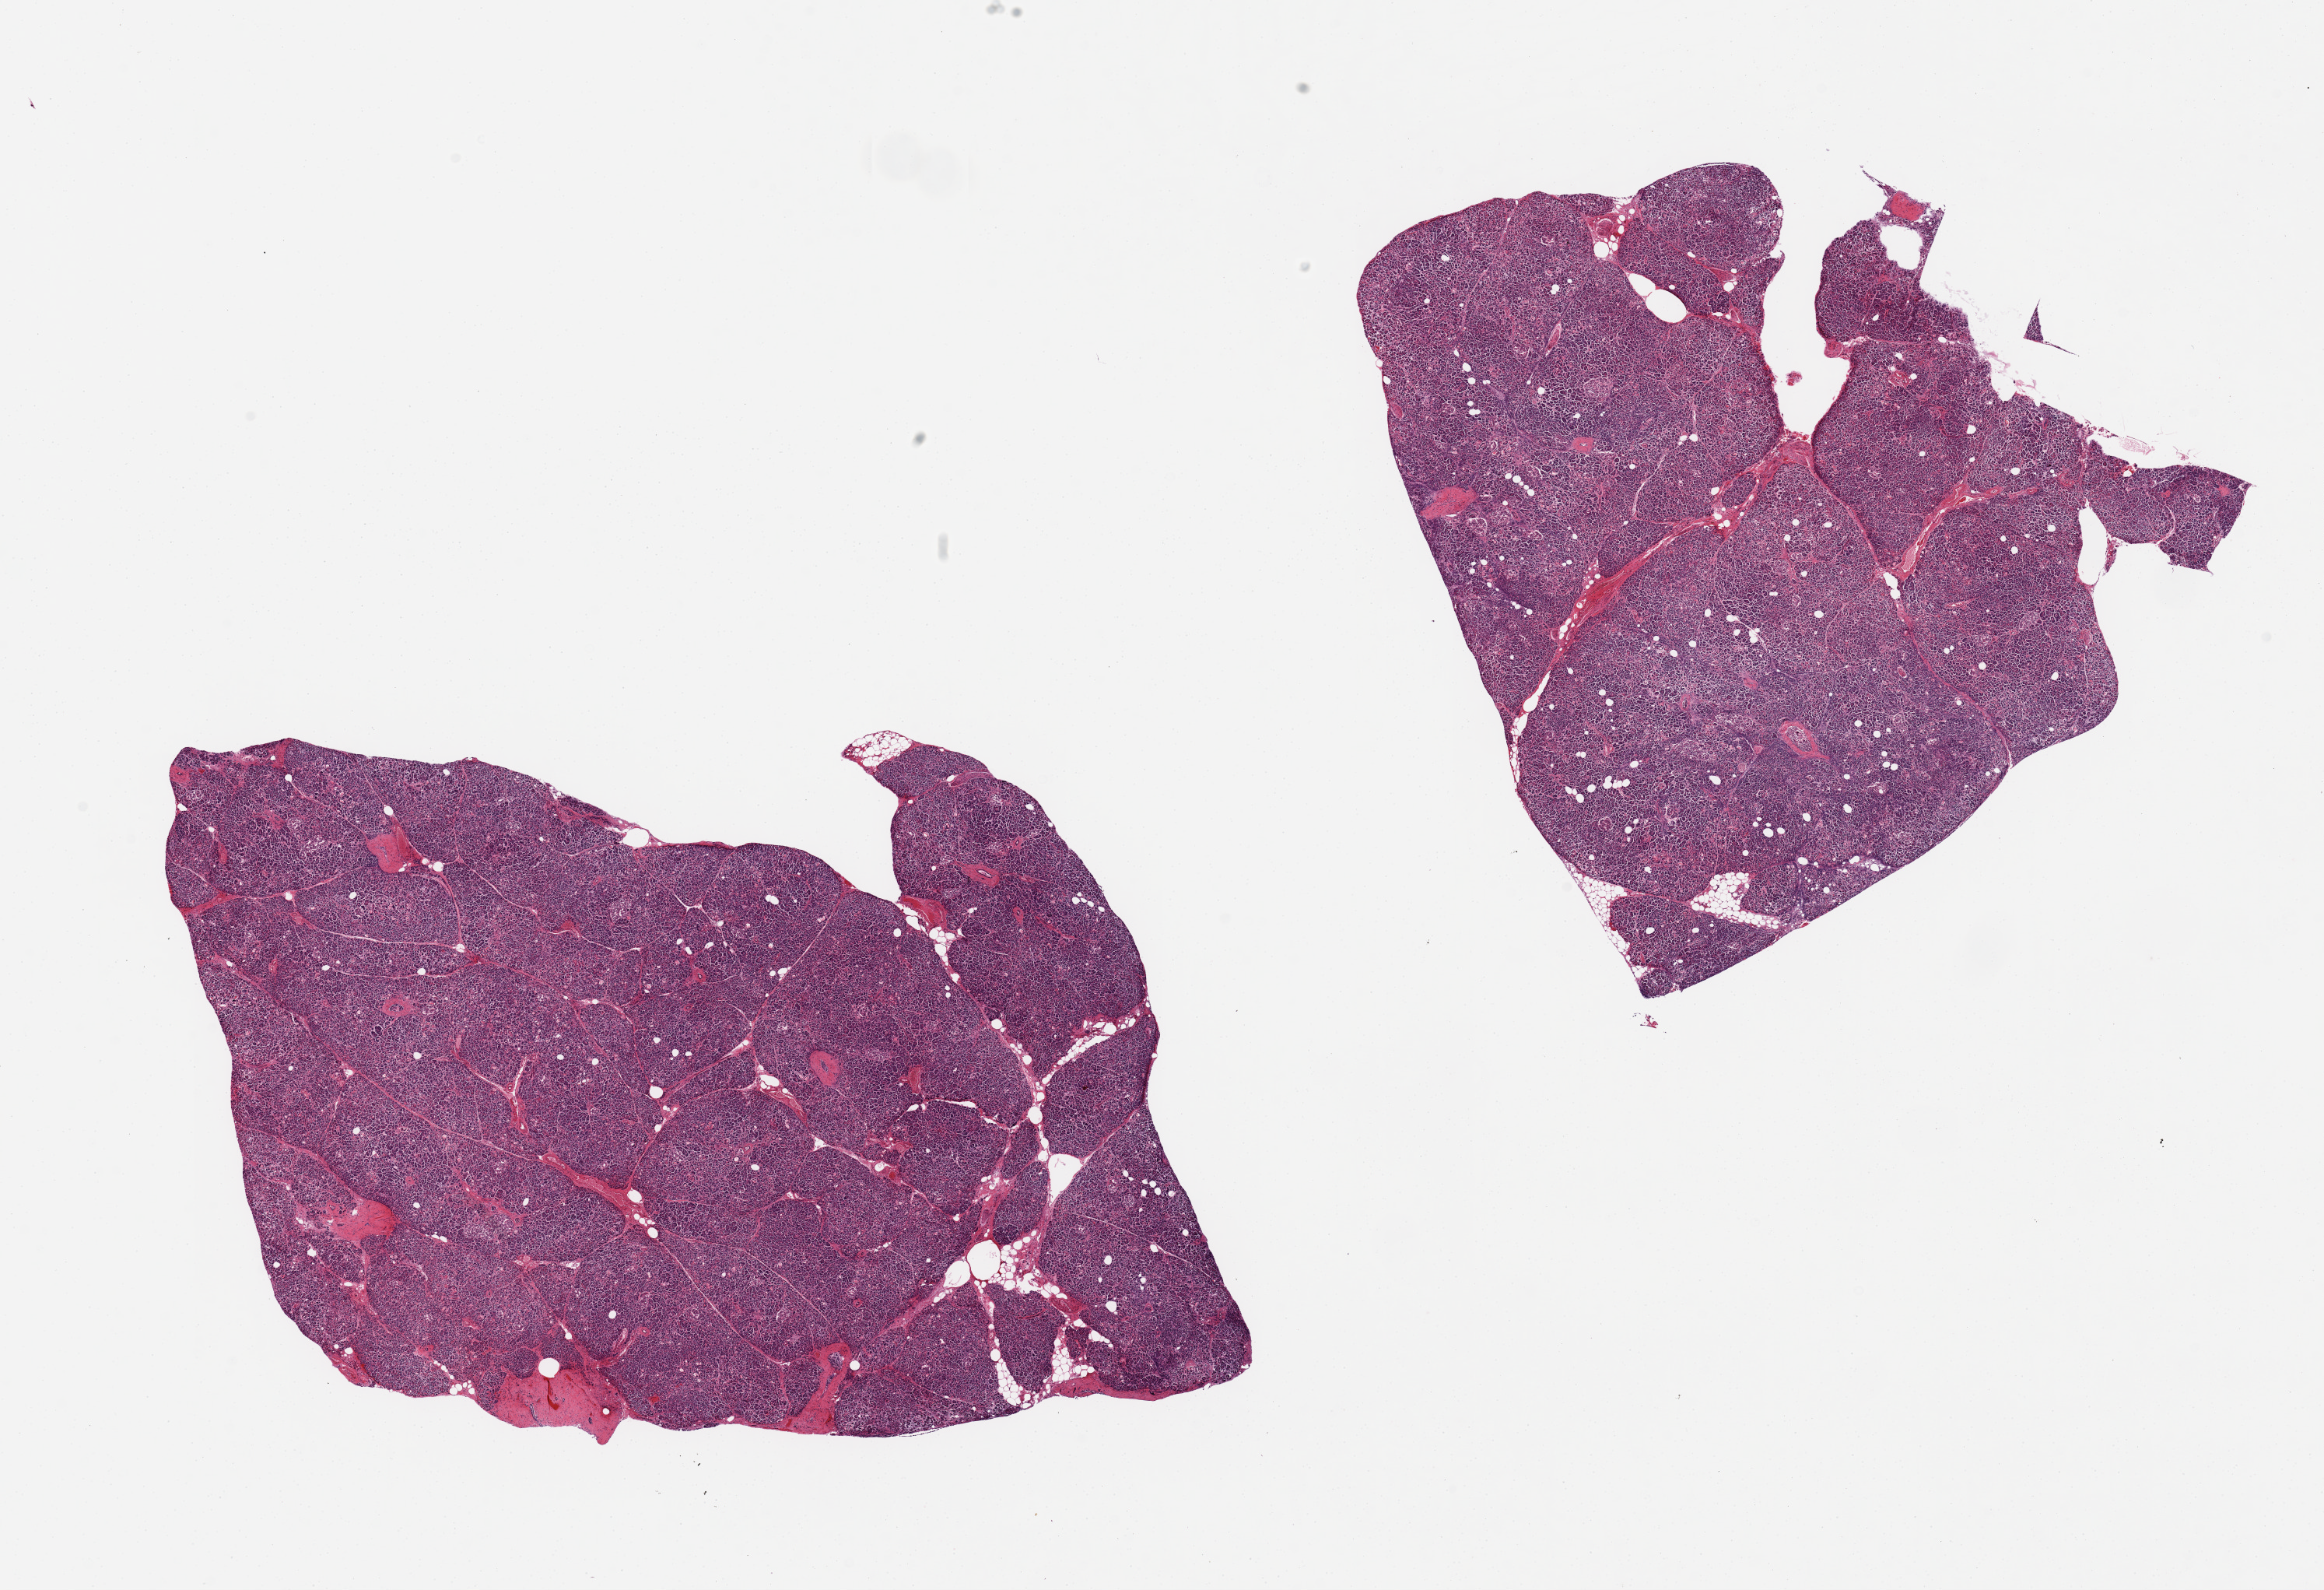
Digitized H&E-stained section, whole scanned area (about 23.6 x 16.2 mm, slide scanned at 20x) shown as a low-resolution overview. PAXgene-fixed, paraffin-embedded tissue. Section of pancreas (target tissue). Tissue donor sample. Male donor.
* pathologist's review note for this sample: 2 pieces, moderate autolysis/saponification; Islets still generally visible